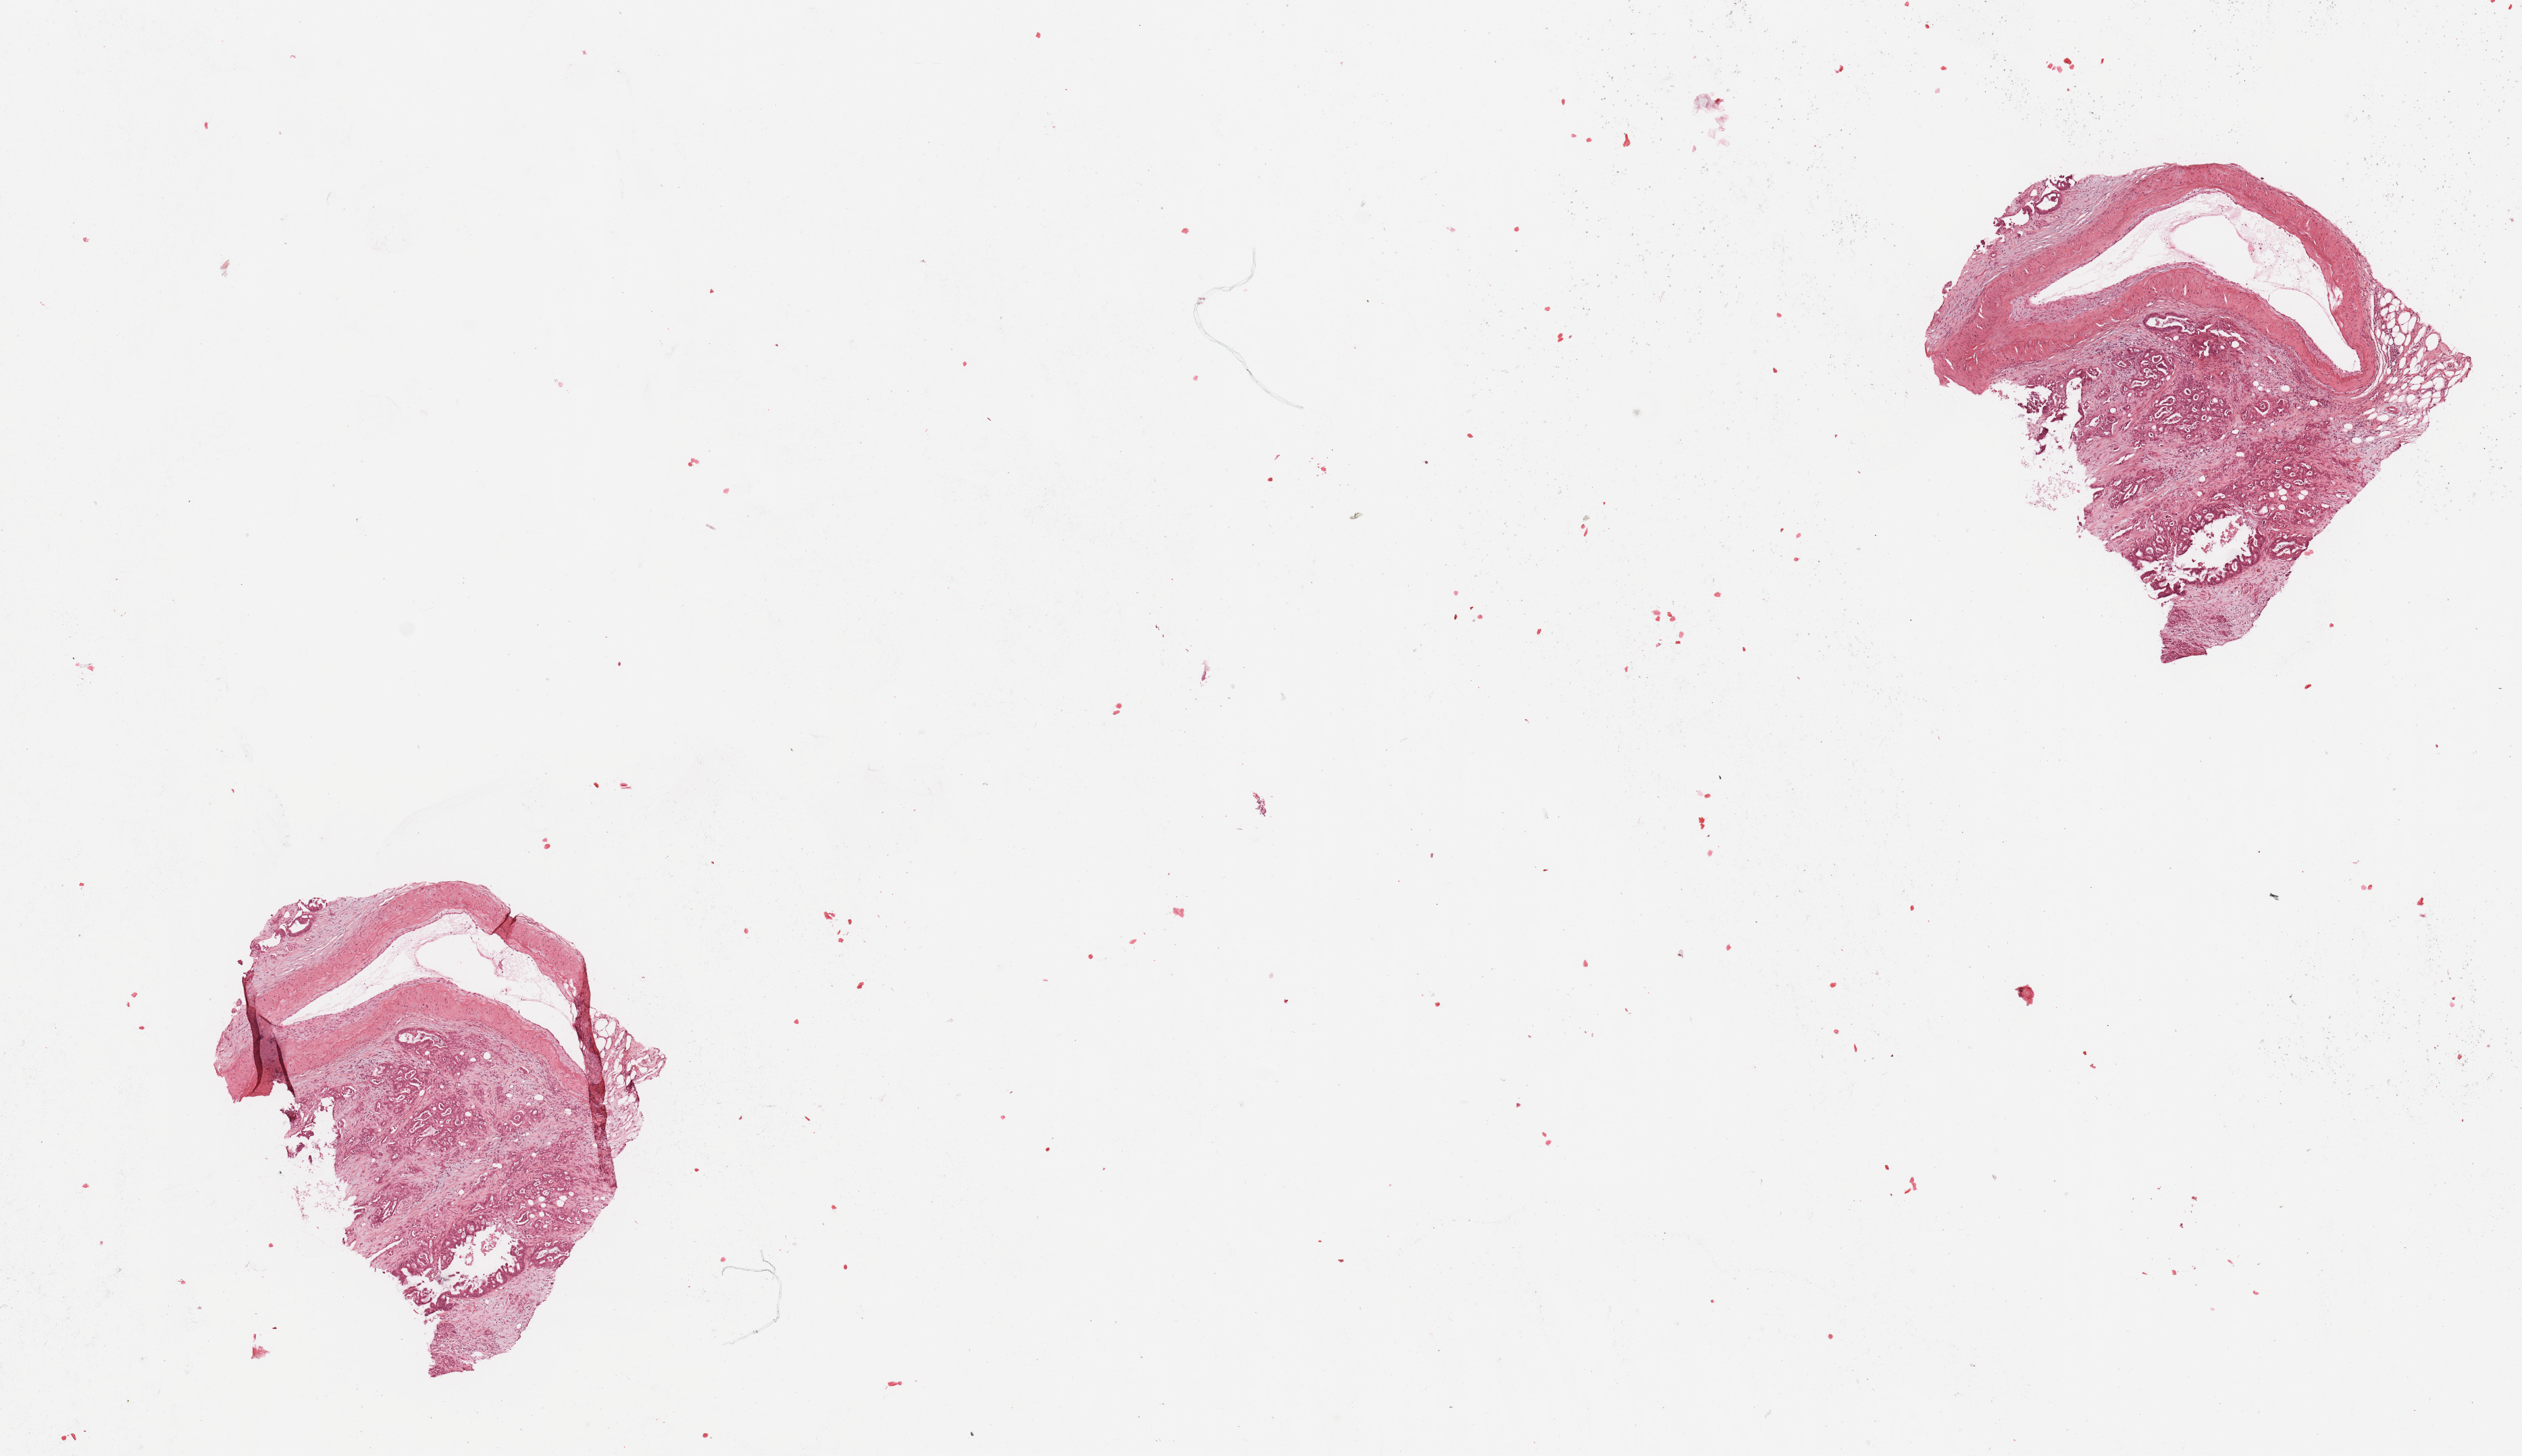
H&E-stained whole-slide image — low-resolution overview of the scanned area, about 14.8 x 8.5 mm (from a 20x scan), pancreas, tumour tissue. Female, 69 y/o. Histologic grade: G2 (moderately differentiated).
* AJCC pathologic stage: IIB
* primary tumour site (as recorded): head
* histologic diagnosis: Infiltrating duct carcinoma, NOS